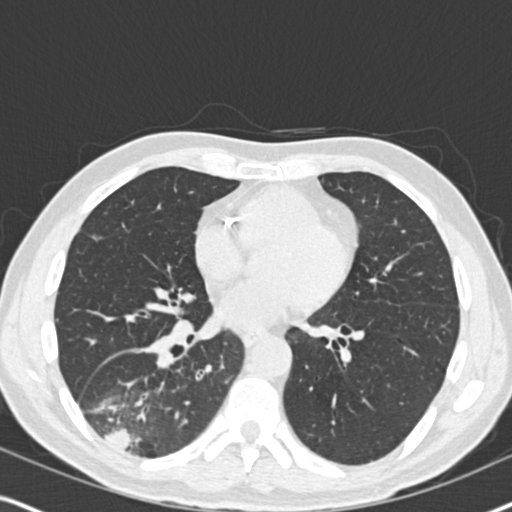
Low-dose screening chest CT, one axial slice. Slice 87 of 182 in the series (ordered by position). 120 kVp. Lung window (W 1500 / L -600 HU). 2 mm slice thickness. 512 × 512 image matrix, field of view 330 × 330 mm.
Outlined on this slice (expert manual segmentation):
- lesion 1 (tumor, lower lobe of right lung): bounding box (x1, y1, x2, y2) in pixels: (104, 426, 134, 450)